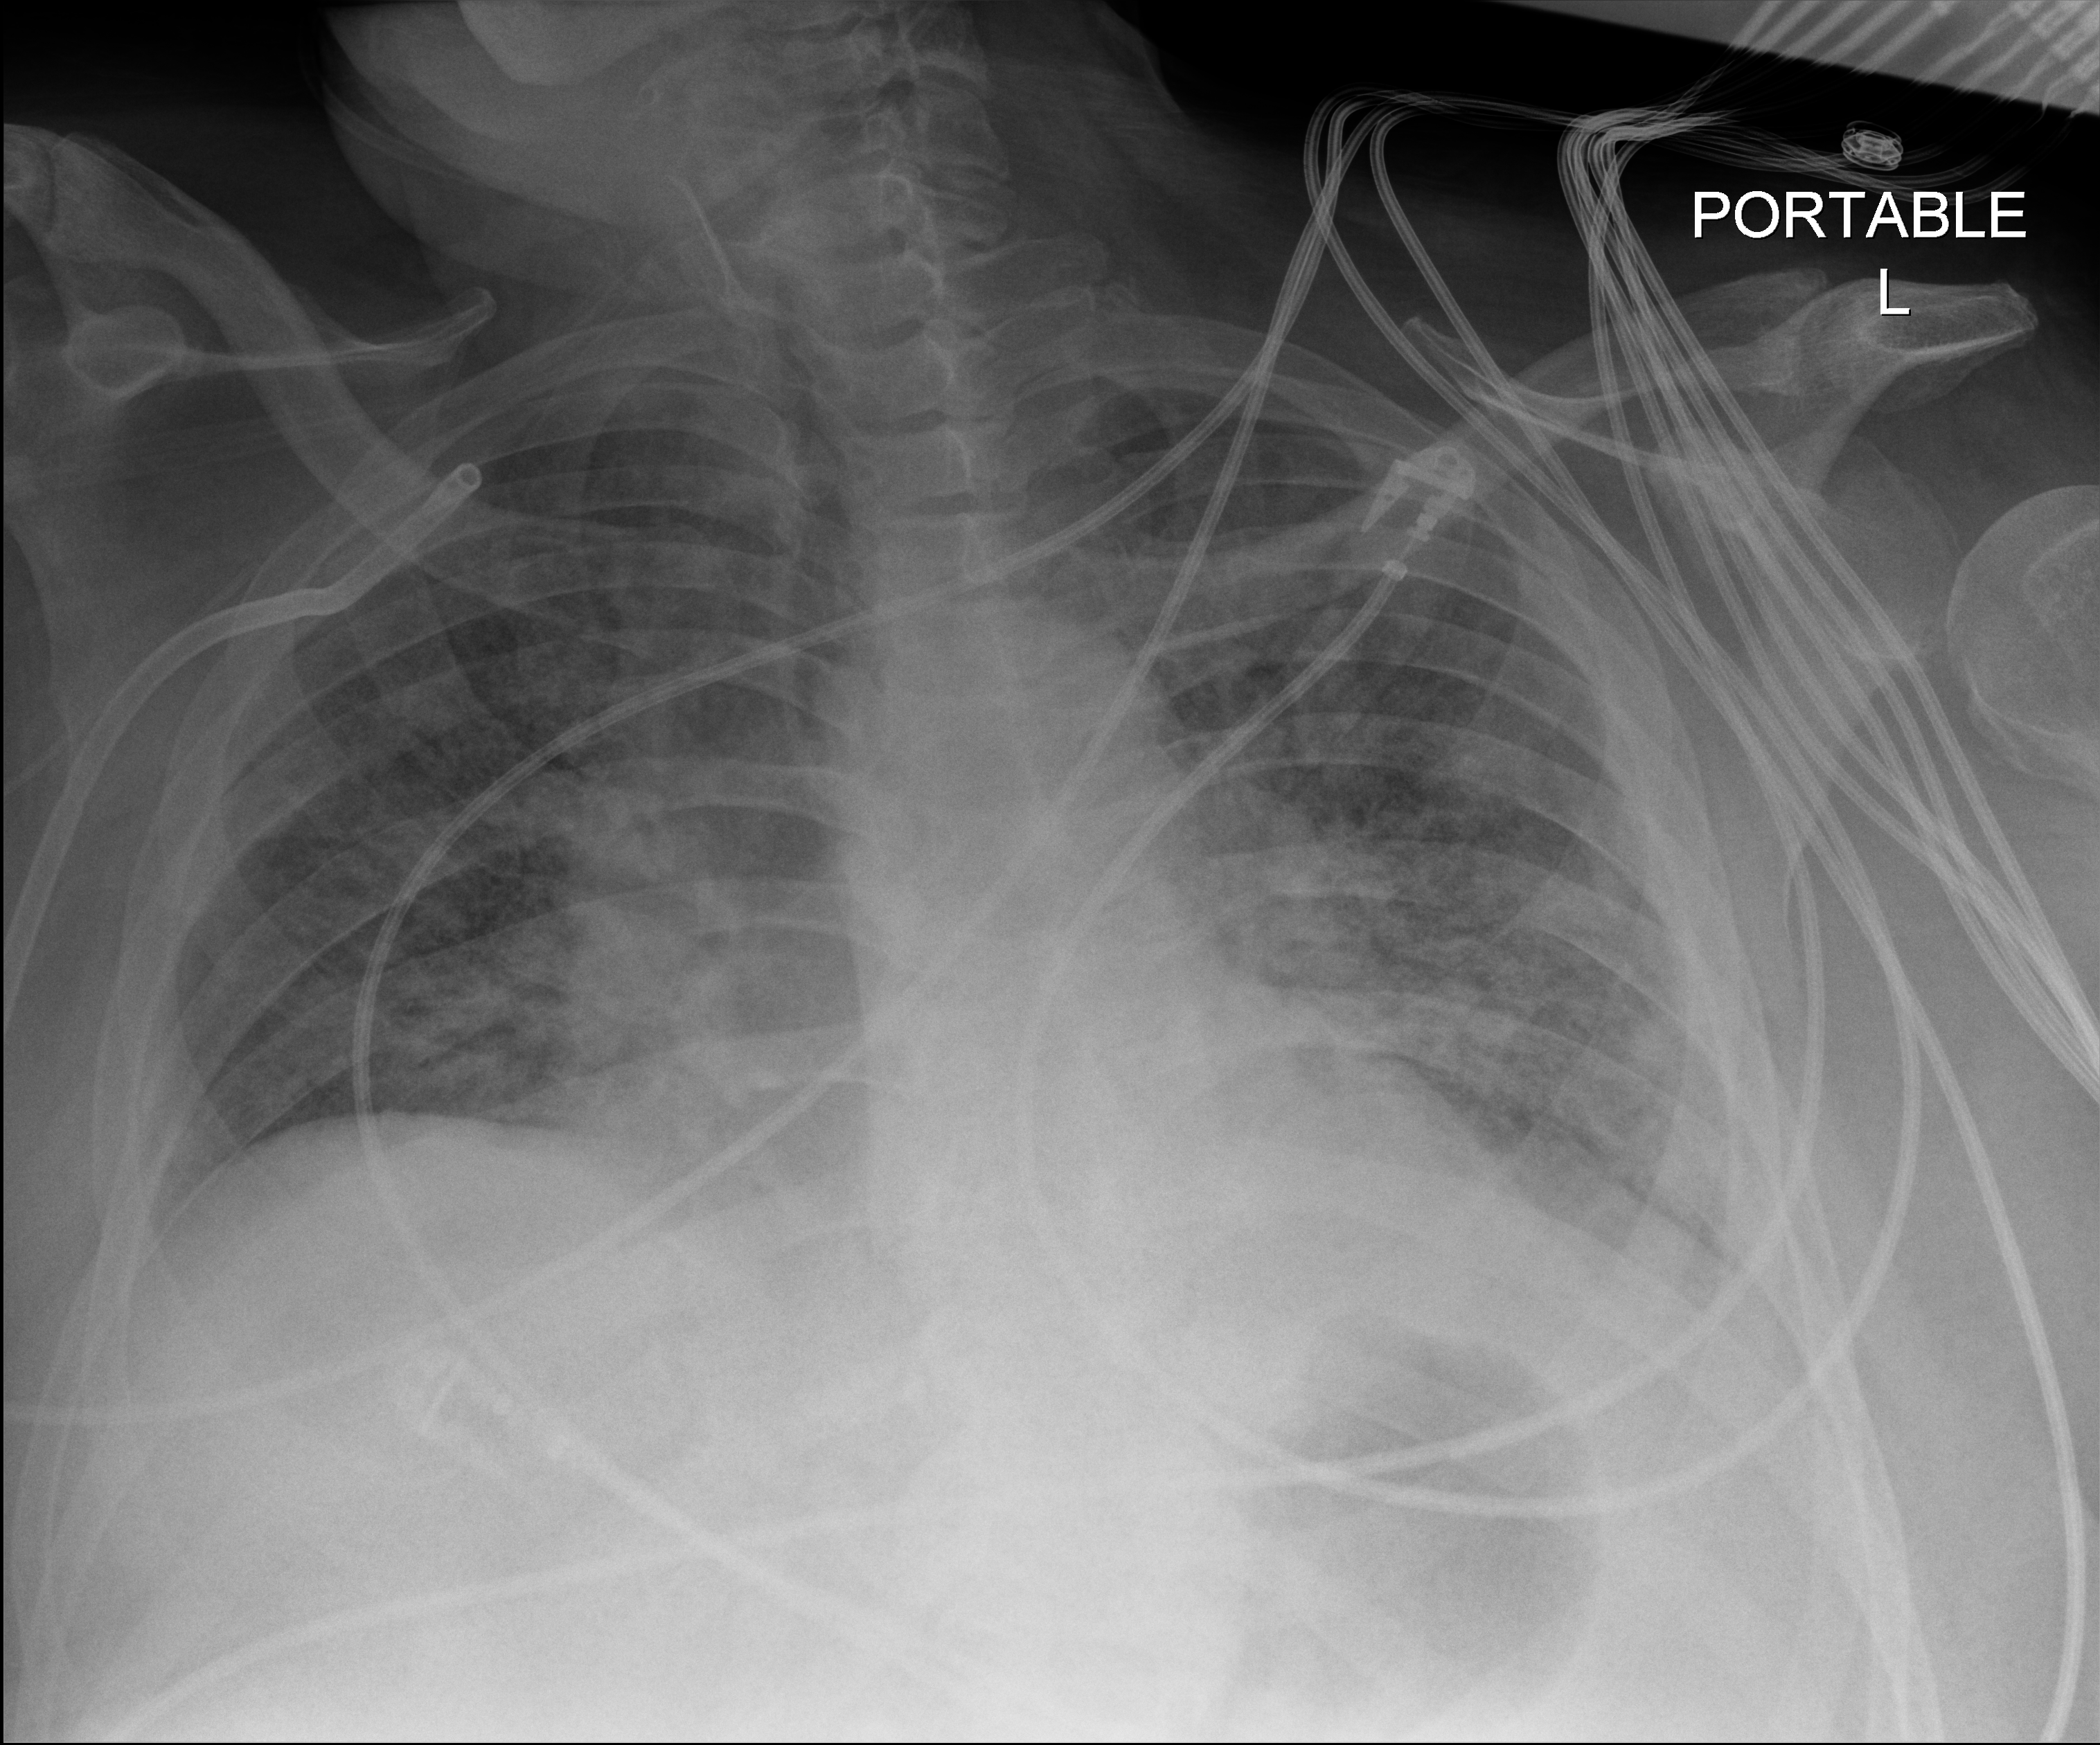
Chest radiograph; anteroposterior (AP) projection. Male patient hospitalised with COVID-19, age 60–74 years.
From the hospital-stay record, not from the radiograph (when in the stay this image was taken is not recorded): mechanically ventilated during this hospital stay: yes; hypertension (admission record): yes; admitted to intensive care during this hospital stay: yes.